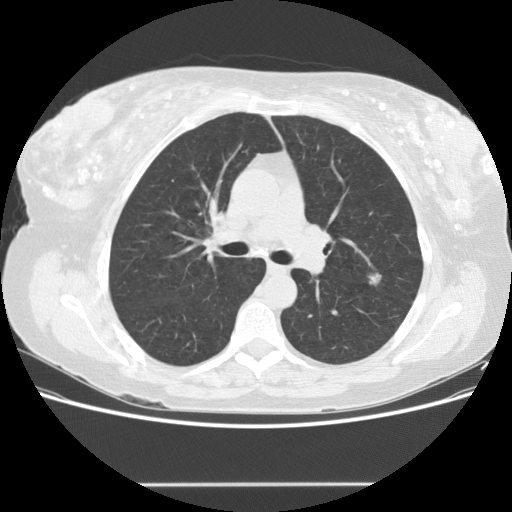
Low-dose screening chest CT, one axial slice. Slice 96 of 151 in the series (ordered by position). Lung window (W 1500 / L -600 HU). 2.5 mm slice thickness. 512 × 512 image matrix, field of view 360 × 360 mm.
Annotated regions visible in this slice (outlined manually by an expert reader):
- lesion 1 (tumor, upper lobe of left lung): box from (x=368, y=273) to (x=382, y=285) px